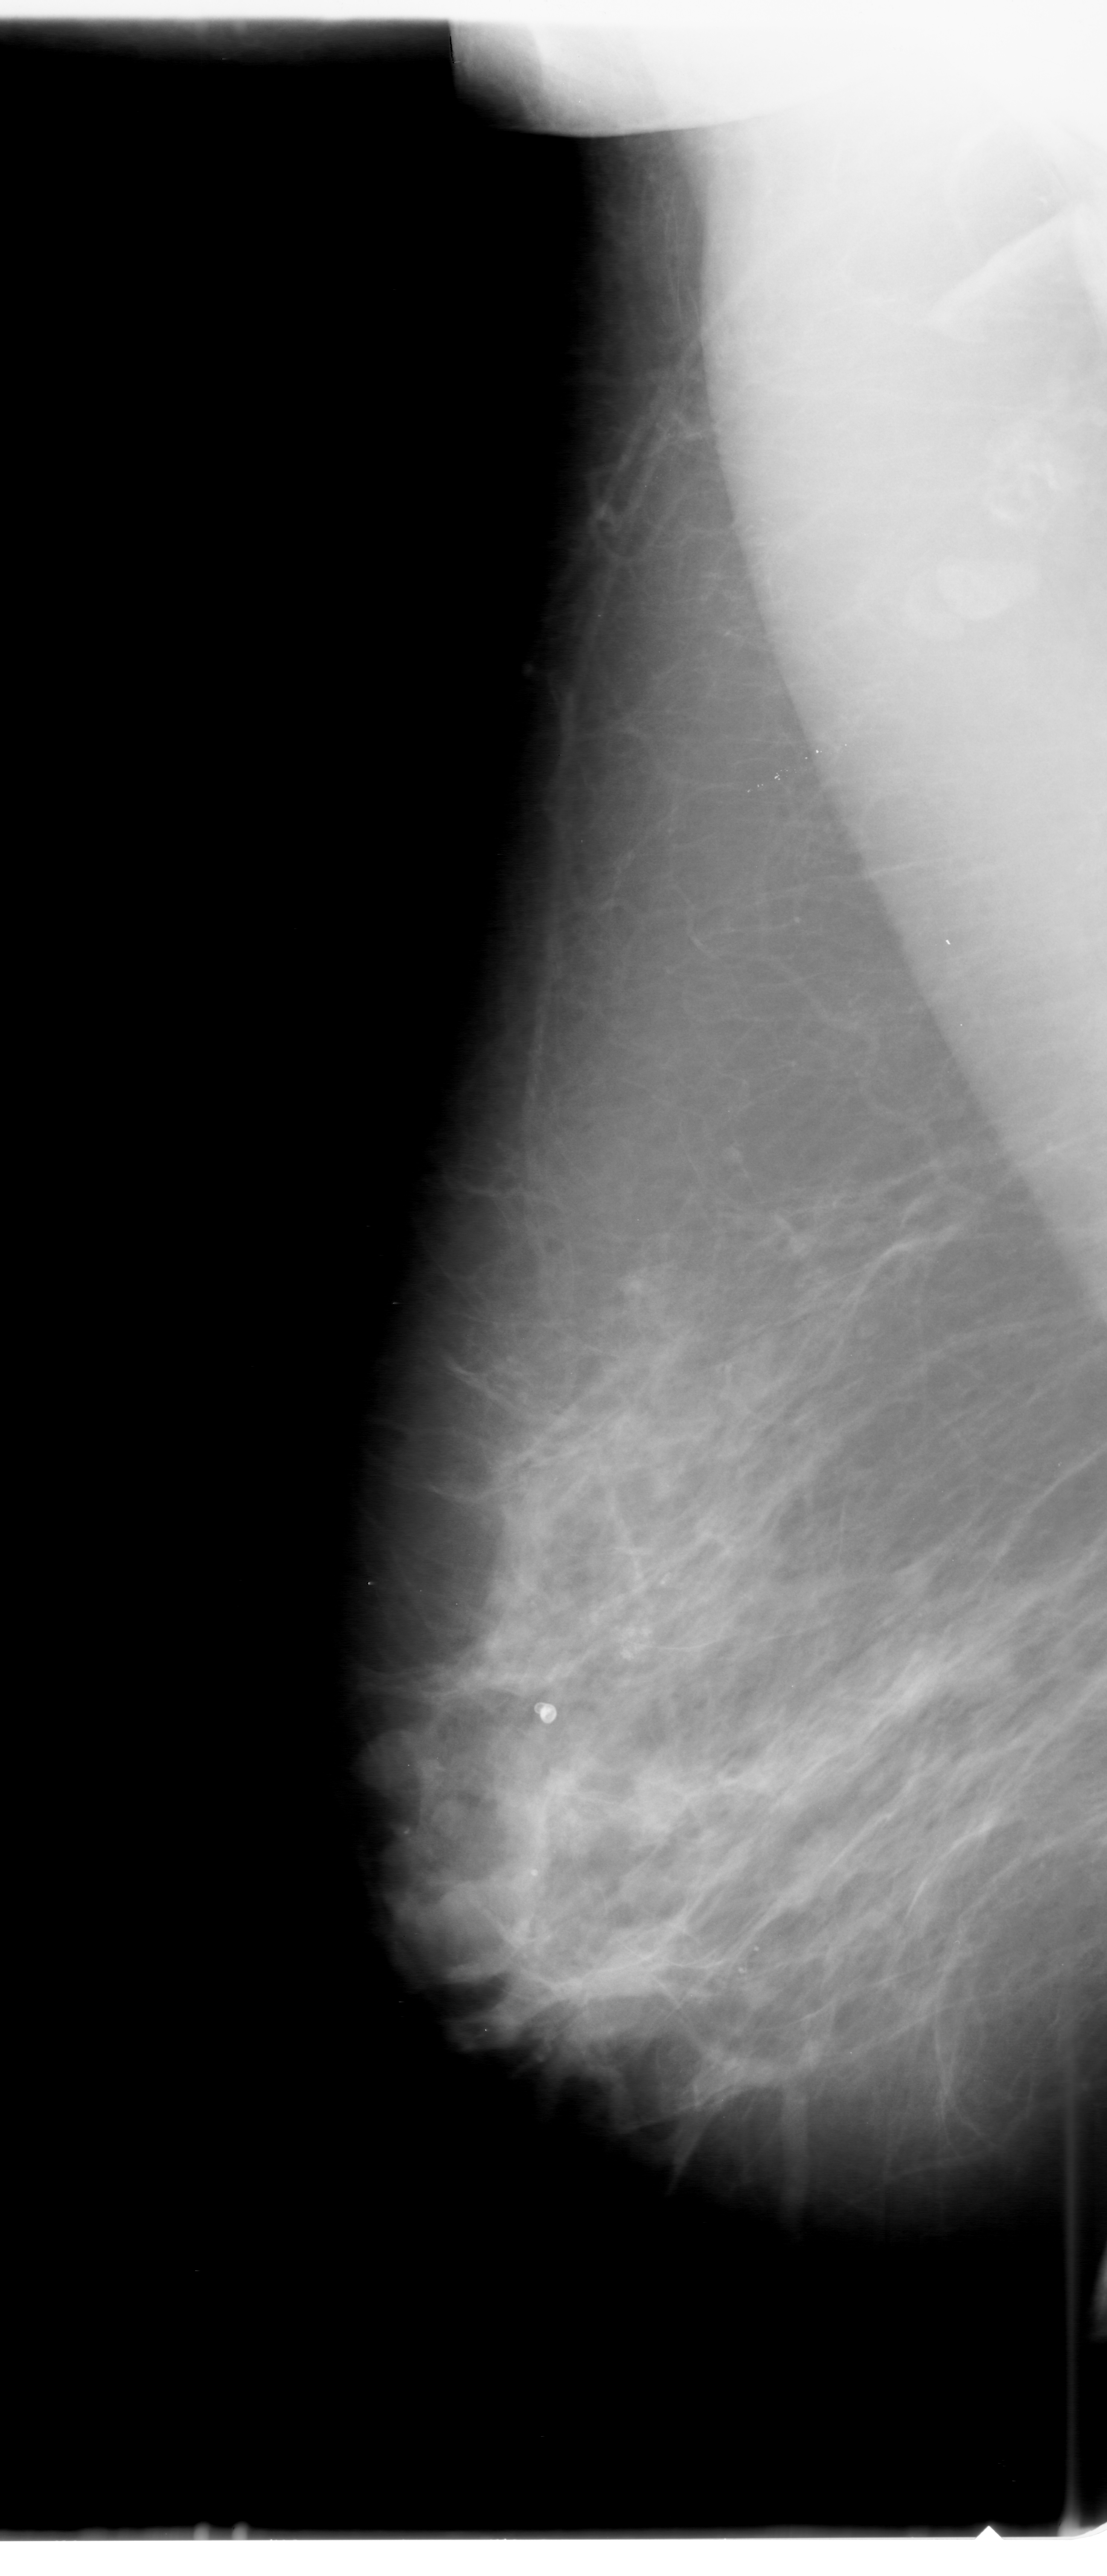
Scanned film-screen mammogram; right breast; MLO view; 1107 × 2576 image matrix.
Marked abnormalities (boxes around the expert regions of interest):
- calcifications, morphology amorphous, distribution clustered; BI-RADS assessment category 3; subtlety rating 3 on a 1 (subtle) to 5 (obvious) scale; pathology (as recorded): malignant: box from (x=549, y=1519) to (x=778, y=1750) px